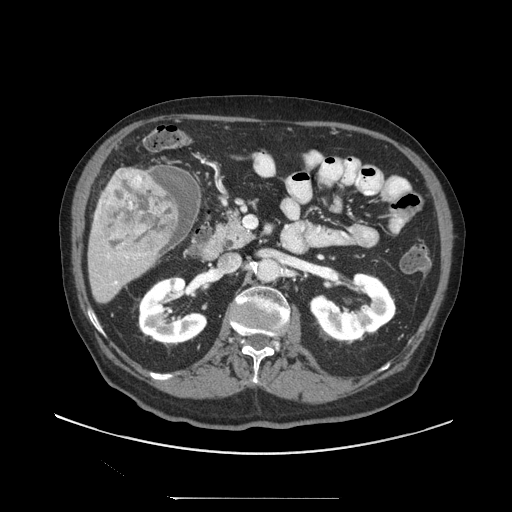
Contrast-enhanced abdominal CT (liver protocol), one axial slice. Position 40 of 97 along the scan axis. 140 kVp. Soft-tissue window (W 400 / L 40 HU). 2.5 mm slice thickness. 512 × 512 image matrix, field of view 450 × 450 mm. From the clinical record (not read from this slice): diagnosis: hepatocellular carcinoma (patient treated with transarterial chemoembolisation; whether this scan precedes or follows treatment is not stated here); TNM stage (as recorded): Stage-IIIC; Child-Pugh class: A.
Outlined on this slice (semi-automatically segmented with operator editing):
- liver parenchyma outside the tumour (the mass and vessels are separate outlines, so this box may not span the whole liver): bounding box [x1, y1, x2, y2] px = [88, 162, 200, 302]
- mass: [100, 171, 178, 254]
- liver vessels: [95, 216, 128, 284]